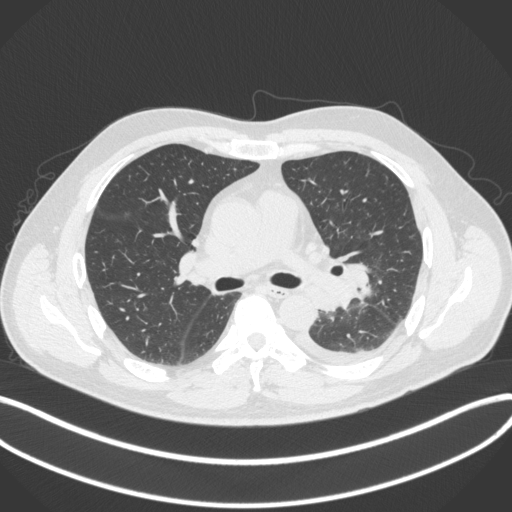
Chest CT, one axial slice; position 216 of 350 along the scan axis; reconstruction kernel B31f; 120 kVp; lung window (W 1500 / L -600 HU); 512 × 512 image matrix. Male patient, age 58 years. Case-level facts recorded for this patient, not image findings: clinical TNM (as recorded): T3 N1 M1b.
Structures marked on this image (rectangle marked by the reading radiologist):
- lung tumour (recorded histology: small cell carcinoma): box from (x=334, y=263) to (x=373, y=311) px